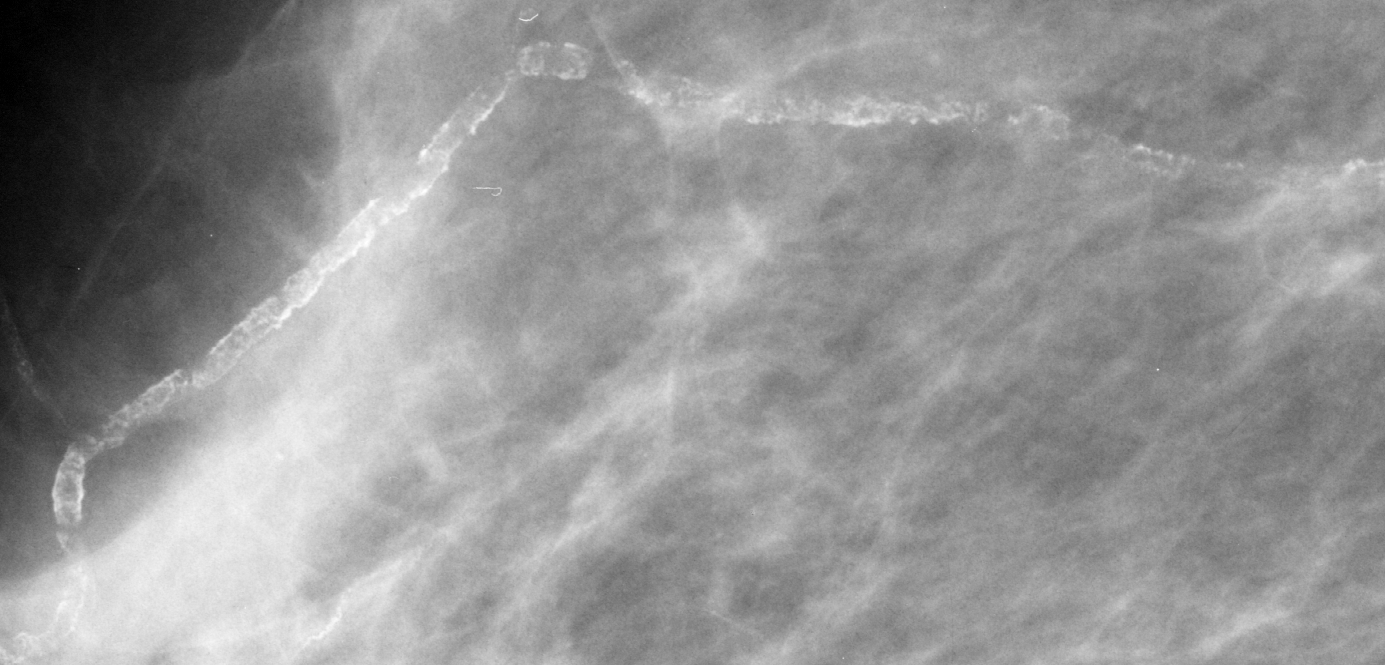
Region of interest cut from a scanned film mammogram (one marked finding), right breast, MLO view.
Finding: calcifications, morphology vascular; BI-RADS assessment category 2; benign; no additional work-up was recommended (benign without callback).